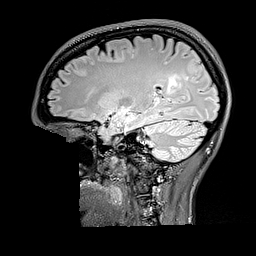
Brain MRI from a brain-tumour surgery series, one sagittal slice; slice 109 of 176 in the series (ordered by position); T2 FLAIR; 1 mm slice thickness; 256 × 256 image matrix, field of view 256 × 256 mm. Case-level facts recorded for this patient, not image findings: histopathology: Oligodendroglioma; WHO grade: 2; IDH mutation: yes; tumour location: Right Parietal.
Outlined on this slice (manually delineated by an expert):
- tumour: box from (x=167, y=75) to (x=182, y=94) px